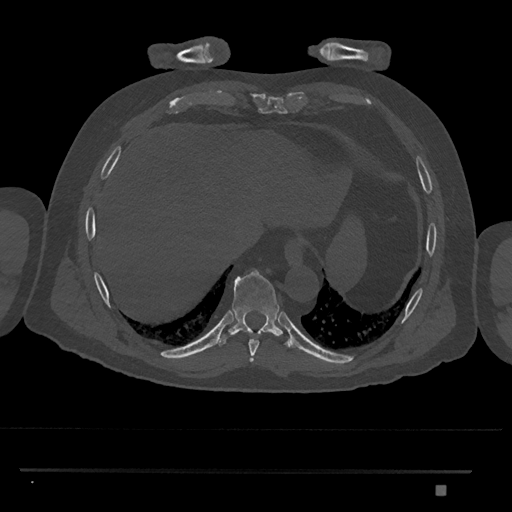
CT including the spine, one axial slice; position 1075 of 1134 along the scan axis; 120 kVp; bone window (W 1800 / L 400 HU); 0.5 mm slice thickness; 512 × 512 image matrix. Patient: male, 65 years. From the clinical record (not read from this slice): primary cancer: prostate.
Structures marked on this image (semi-automatically segmented with operator editing):
- T8 vertebra: bounding box <248,340,259,362> (left, top, right, bottom; pixels)
- T9 vertebra: <216,270,292,349>